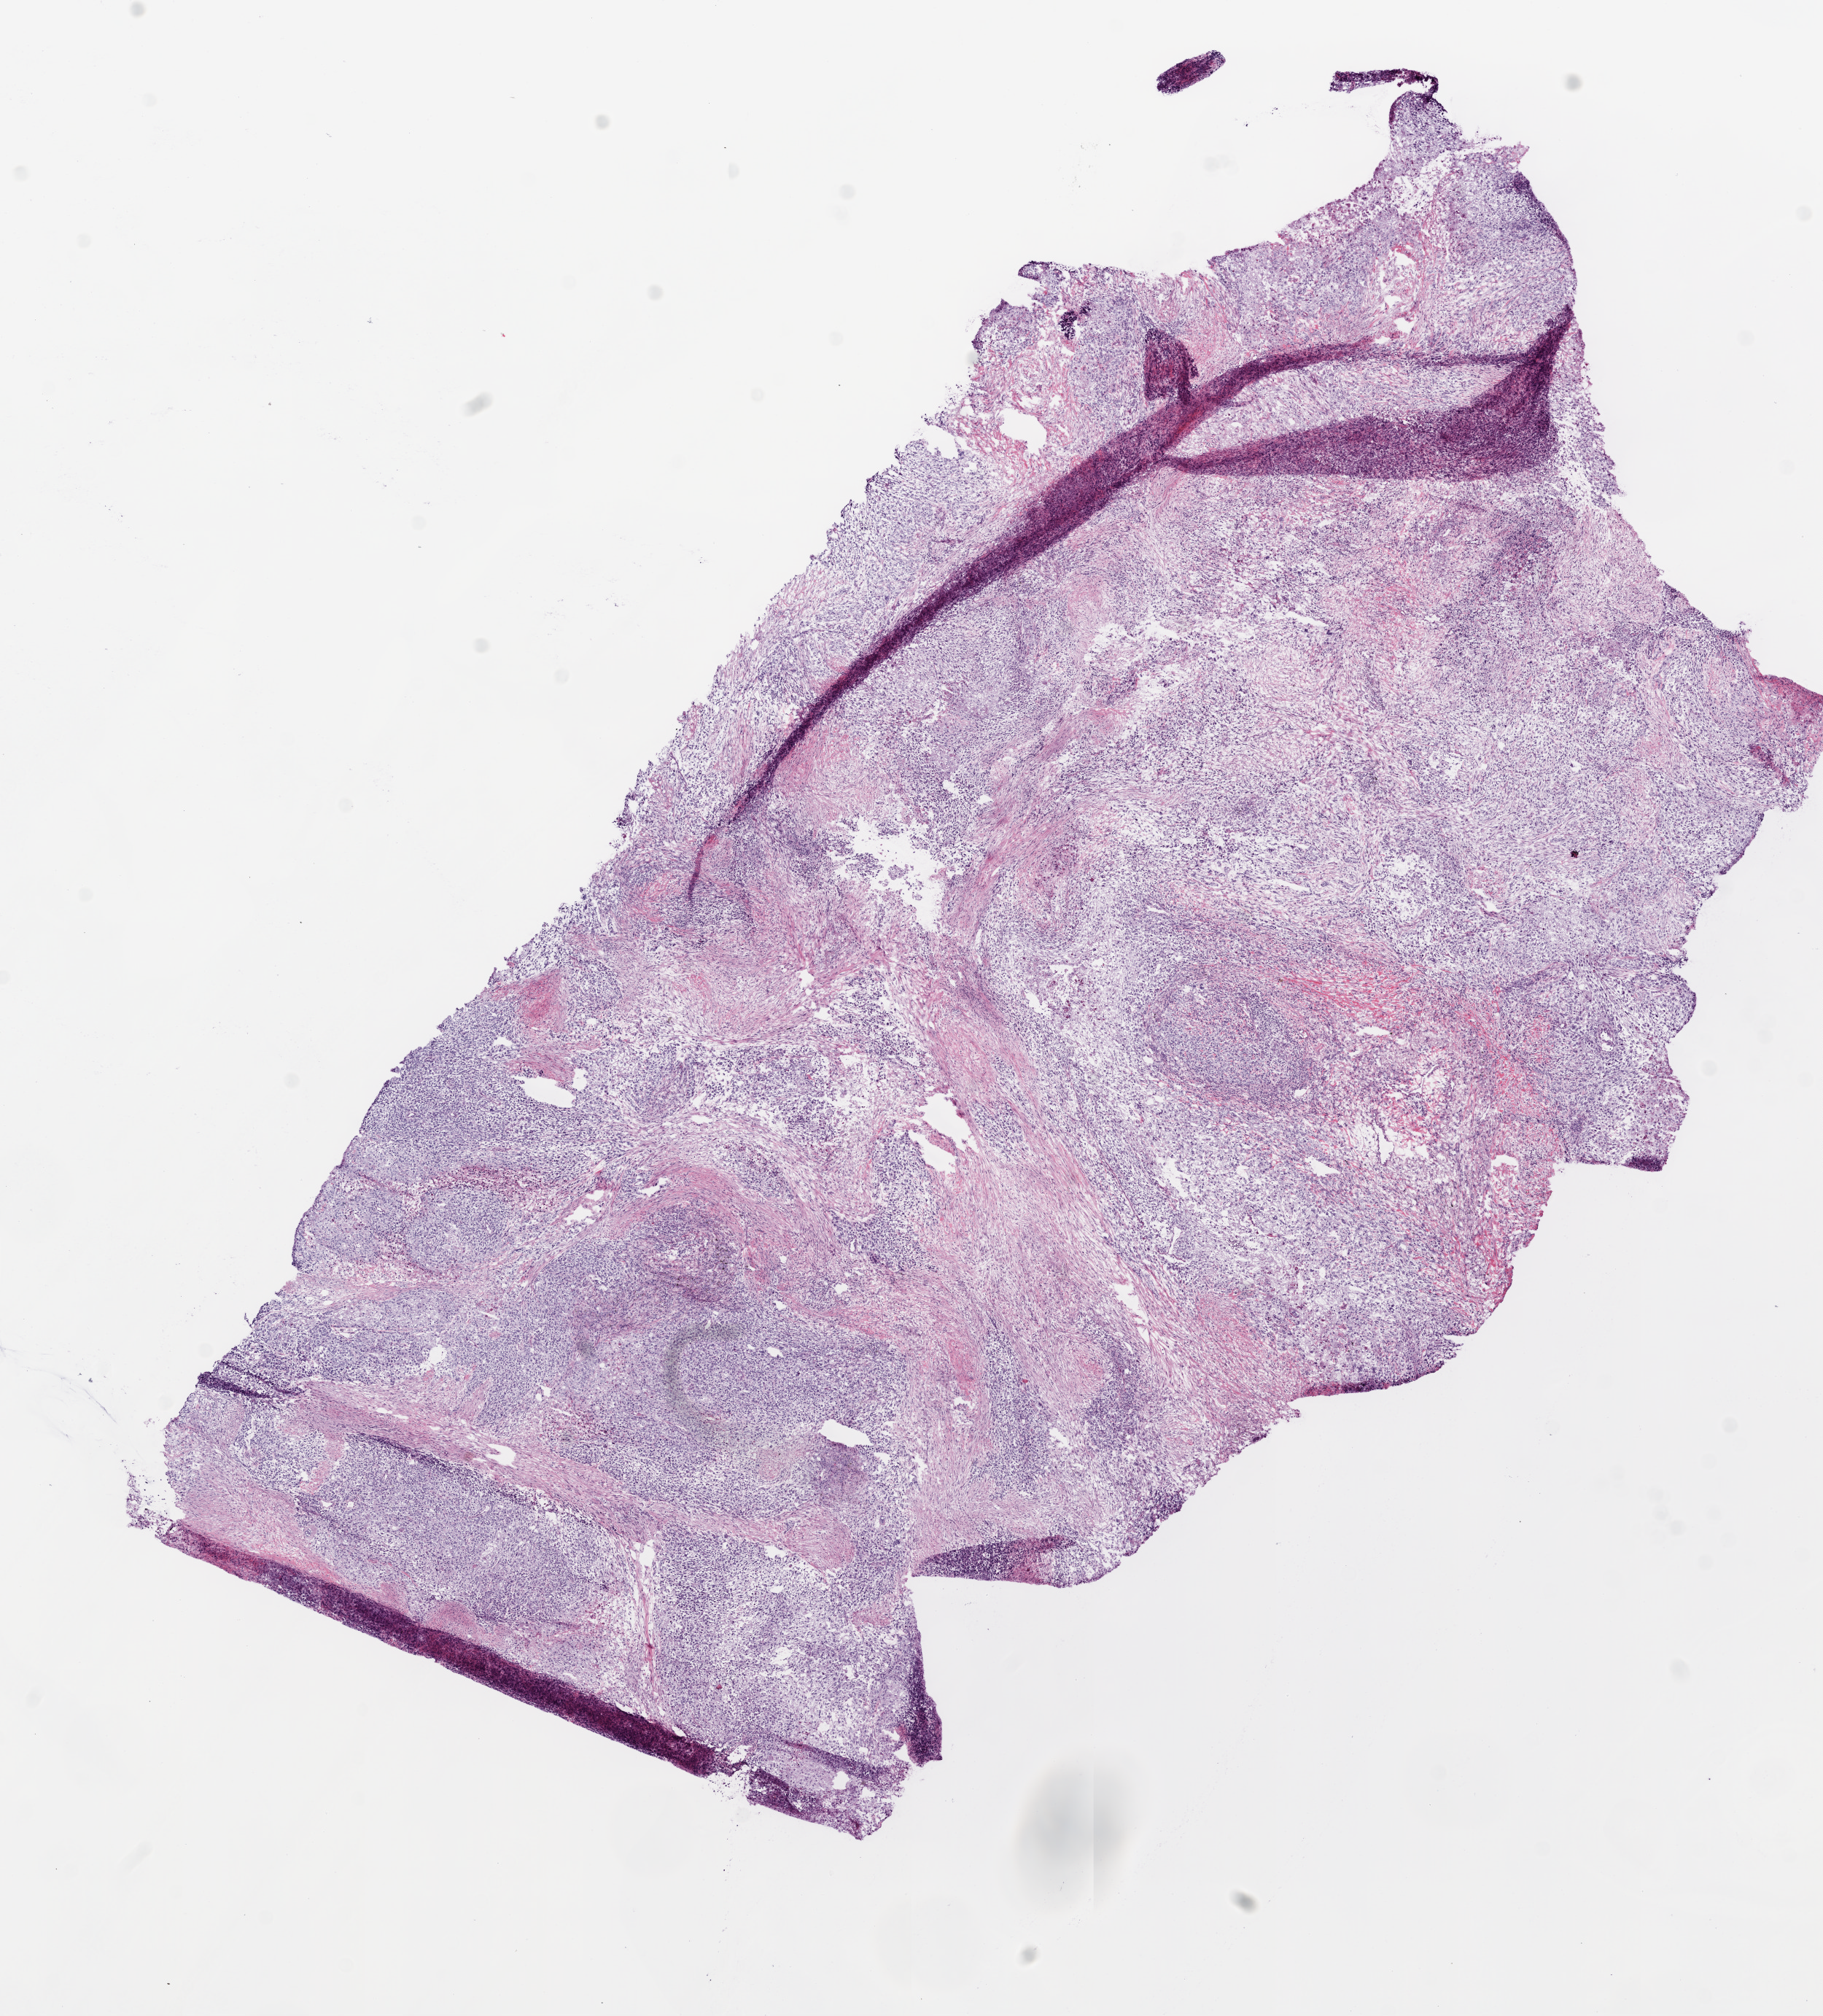
Hematoxylin and eosin (H&E) stained whole-slide image — whole scanned area (about 10.0 x 11.1 mm, slide scanned at 20x) shown as a low-resolution overview; frozen section from the bottom of the tissue portion; lung, primary tumour sample. Patient: male, age at initial diagnosis 71 years. Slide review estimates, as recorded: tumour cells 80%, tumour nuclei 80%, normal cells 0%, stromal cells 18%, necrosis 2%. Inflammatory infiltration, as recorded: lymphocyte infiltration 5%, neutrophil infiltration 5%.
- histologic diagnosis: Squamous cell carcinoma, NOS (upper lobe, lung)
- laterality: right
- AJCC pathologic stage: IB